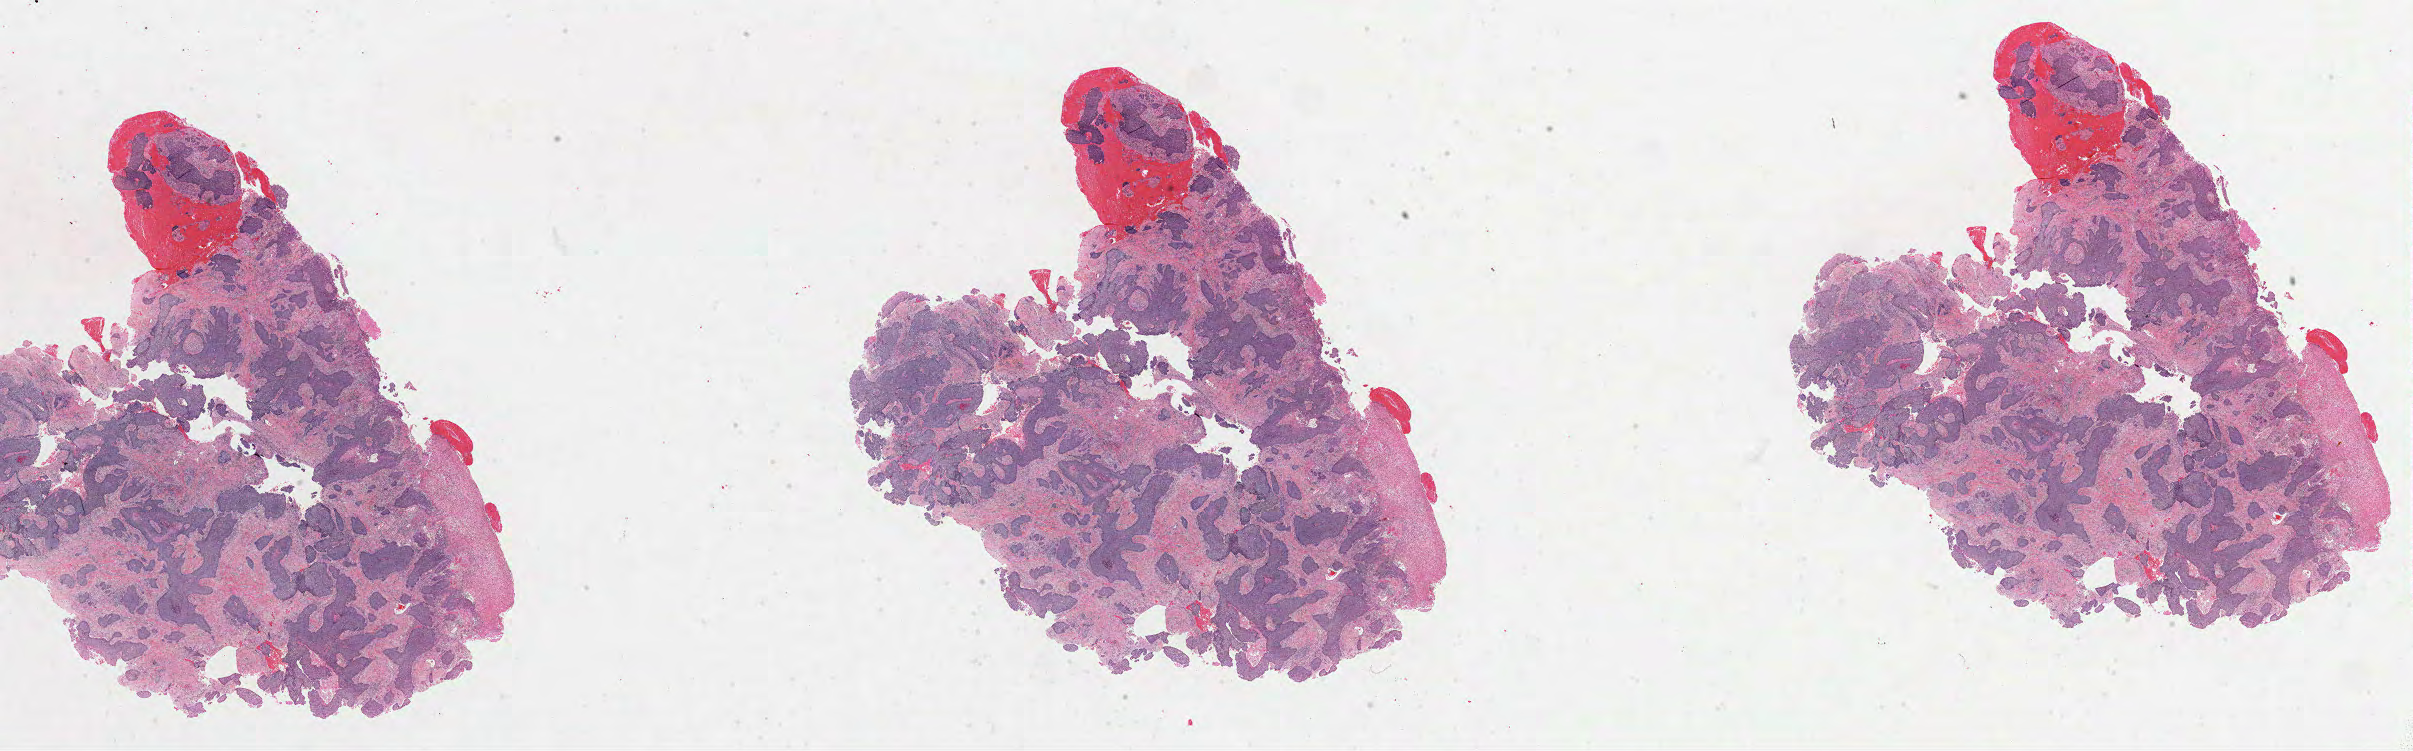
H&E-stained whole-slide image, low-resolution overview of the scanned area, about 38.9 x 12.1 mm. Formalin-fixed paraffin-embedded (FFPE) diagnostic section. Head and neck, primary tumour sample. Patient: male, age at initial diagnosis 83 years. Histologic grade: G2 (moderately differentiated).
Pathologic diagnosis: Squamous cell carcinoma, NOS.